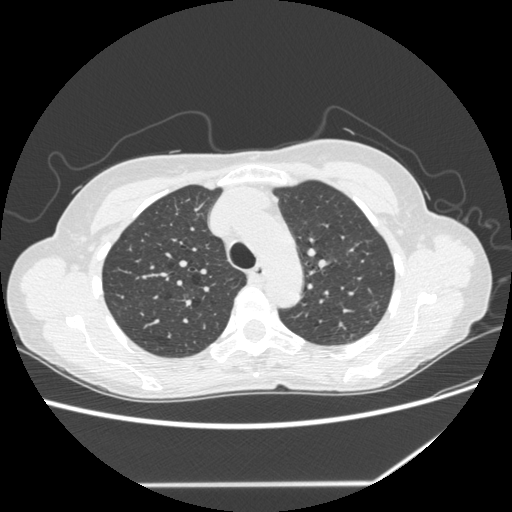
Chest CT (low-dose screening protocol), one axial image; second screening round (one year after baseline); lung window (W 1500 / L -600 HU); 1.25 mm slice thickness; slice 59 of 255 in the series; 512 × 512 image matrix. Female, age 61 years at enrolment.
Lesion marked by an expert reader, bounding box <353,292,389,322> (left, top, right, bottom; pixels). Screening reader's record for this exam (one nodule recorded; not confirmed to be the boxed lesion): non-calcified nodule or mass ≥4 mm, left upper lobe, 8 × 7 mm, poorly defined margins, mixed attenuation, pre-existing on the prior screen: yes; interval growth: yes. Lung cancer was diagnosed 113 days after this screen: bronchiolo-alveolar adenocarcinoma, NOS, left upper lobe, well differentiated (G1), stage IA (AJCC 6th edition), 8 mm at pathology.